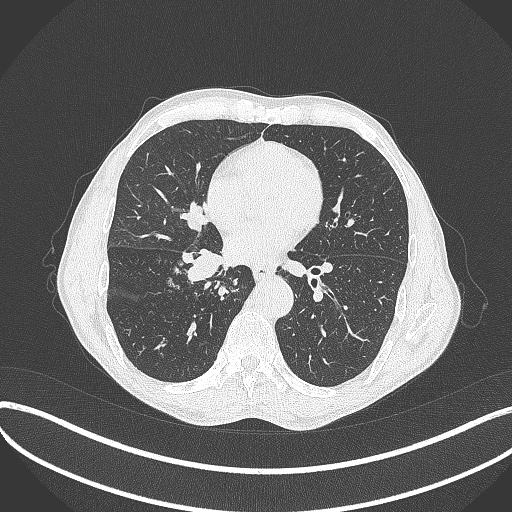
Chest CT, one axial slice. Slice 194 of 481 in the series (ordered by position). Lung window (W 1500 / L -600 HU). 1 mm slice thickness. 512 × 512 image matrix, field of view 400 × 400 mm. Patient: male, 65 years. From the clinical record (not read from this slice): clinical TNM (as recorded): T2a N0 M0; histopathological grade: G2.
Outlined on this slice (bounding box drawn by a radiologist):
- lung tumour (recorded histology: squamous cell carcinoma): bounding box (x1, y1, x2, y2) in pixels: (169, 242, 224, 286)